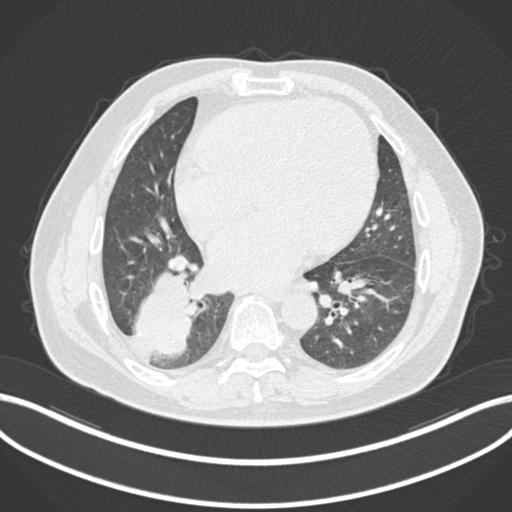
Chest CT, one axial slice; position 65 of 200 along the scan axis; reconstruction kernel B30f; 120 kVp; lung window (W 1500 / L -600 HU); 512 × 512 image matrix, field of view 400 × 400 mm. Patient: male, 59 years.
Outlined on this slice (rectangle marked by the reading radiologist):
- lung tumour (recorded histology: adenocarcinoma): box from (x=125, y=267) to (x=197, y=359) px